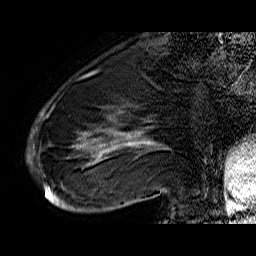
Breast MRI (dynamic contrast-enhanced), one sagittal slice; position 16 of 60 along the scan axis; dynamic contrast-enhanced series, time point 2 of 6 at this slice position (early post-contrast); 1.5 T; TE 6.4 ms, TR 32.9 ms; 4 mm slice thickness; 256 × 256 image matrix, field of view 200 × 200 mm. Female patient. Case-level facts recorded for this patient, not image findings: setting: breast cancer imaged before/during neoadjuvant chemotherapy; receptor status: HR-positive, HER2-negative.
Outlined on this slice (semi-automatic segmentation, software-assisted and operator-edited):
- analysis volume of interest (the breast-tissue region the enhancement analysis was run in; not a lesion): bounding box [x1, y1, x2, y2] px = [44, 74, 176, 210]
- tumour enhancement mask (voxels above the 100 % enhancement threshold inside the analysis volume of interest): [44, 132, 166, 207]